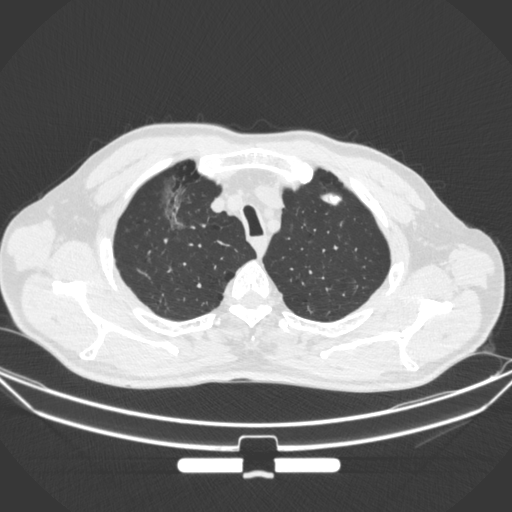
Chest CT, one axial slice; slice 291 of 355 in the series (ordered by position); 120 kVp; lung window (W 1500 / L -600 HU); 1 mm slice thickness; 512 × 512 image matrix, field of view 399 × 399 mm. Male patient, age 67 years. From the clinical record (not read from this slice): clinical TNM (as recorded): T1c N0 M0.
Annotated regions visible in this slice (bounding box drawn by a radiologist):
- lung tumour (recorded histology: adenocarcinoma): bounding box (x1, y1, x2, y2) in pixels: (157, 177, 199, 237)